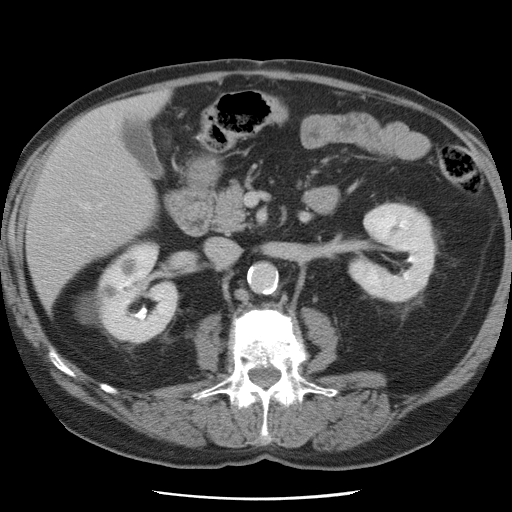
Contrast-enhanced abdominal CT, one axial slice; position 31 of 78 along the scan axis; 120 kVp; intravenous contrast given; soft-tissue window (W 400 / L 40 HU); 5 mm slice thickness; 512 × 512 image matrix, field of view 337 × 337 mm. Male patient, age 75 years. From the clinical record (not read from this slice): diagnosis: colorectal cancer liver metastases, imaged before liver resection; multiple liver metastases: yes; largest metastasis: 2.4 cm; disease in both lobes: yes.
Annotated regions visible in this slice (expert manual segmentation):
- hepatic veins: bounding box [x1, y1, x2, y2] px = [64, 203, 101, 232]
- liver: [28, 94, 164, 305]
- planned liver remnant (the part of the liver to remain after resection): [28, 116, 157, 304]